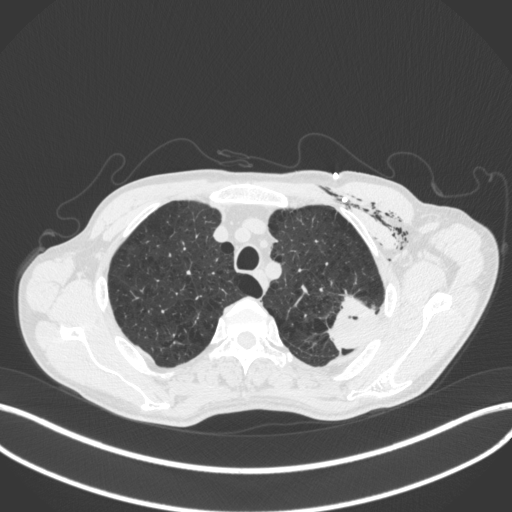
Chest CT, one axial slice. Slice 336 of 416 in the series (ordered by position). 120 kVp. Lung window (W 1500 / L -600 HU). 512 × 512 image matrix. Patient: male, 58 years. From the clinical record (not read from this slice): clinical TNM (as recorded): T3 N0 M0.
Structures marked on this image (bounding box drawn by a radiologist):
- lung tumour (recorded histology: adenocarcinoma): bounding box (x1, y1, x2, y2) in pixels: (320, 287, 381, 349)